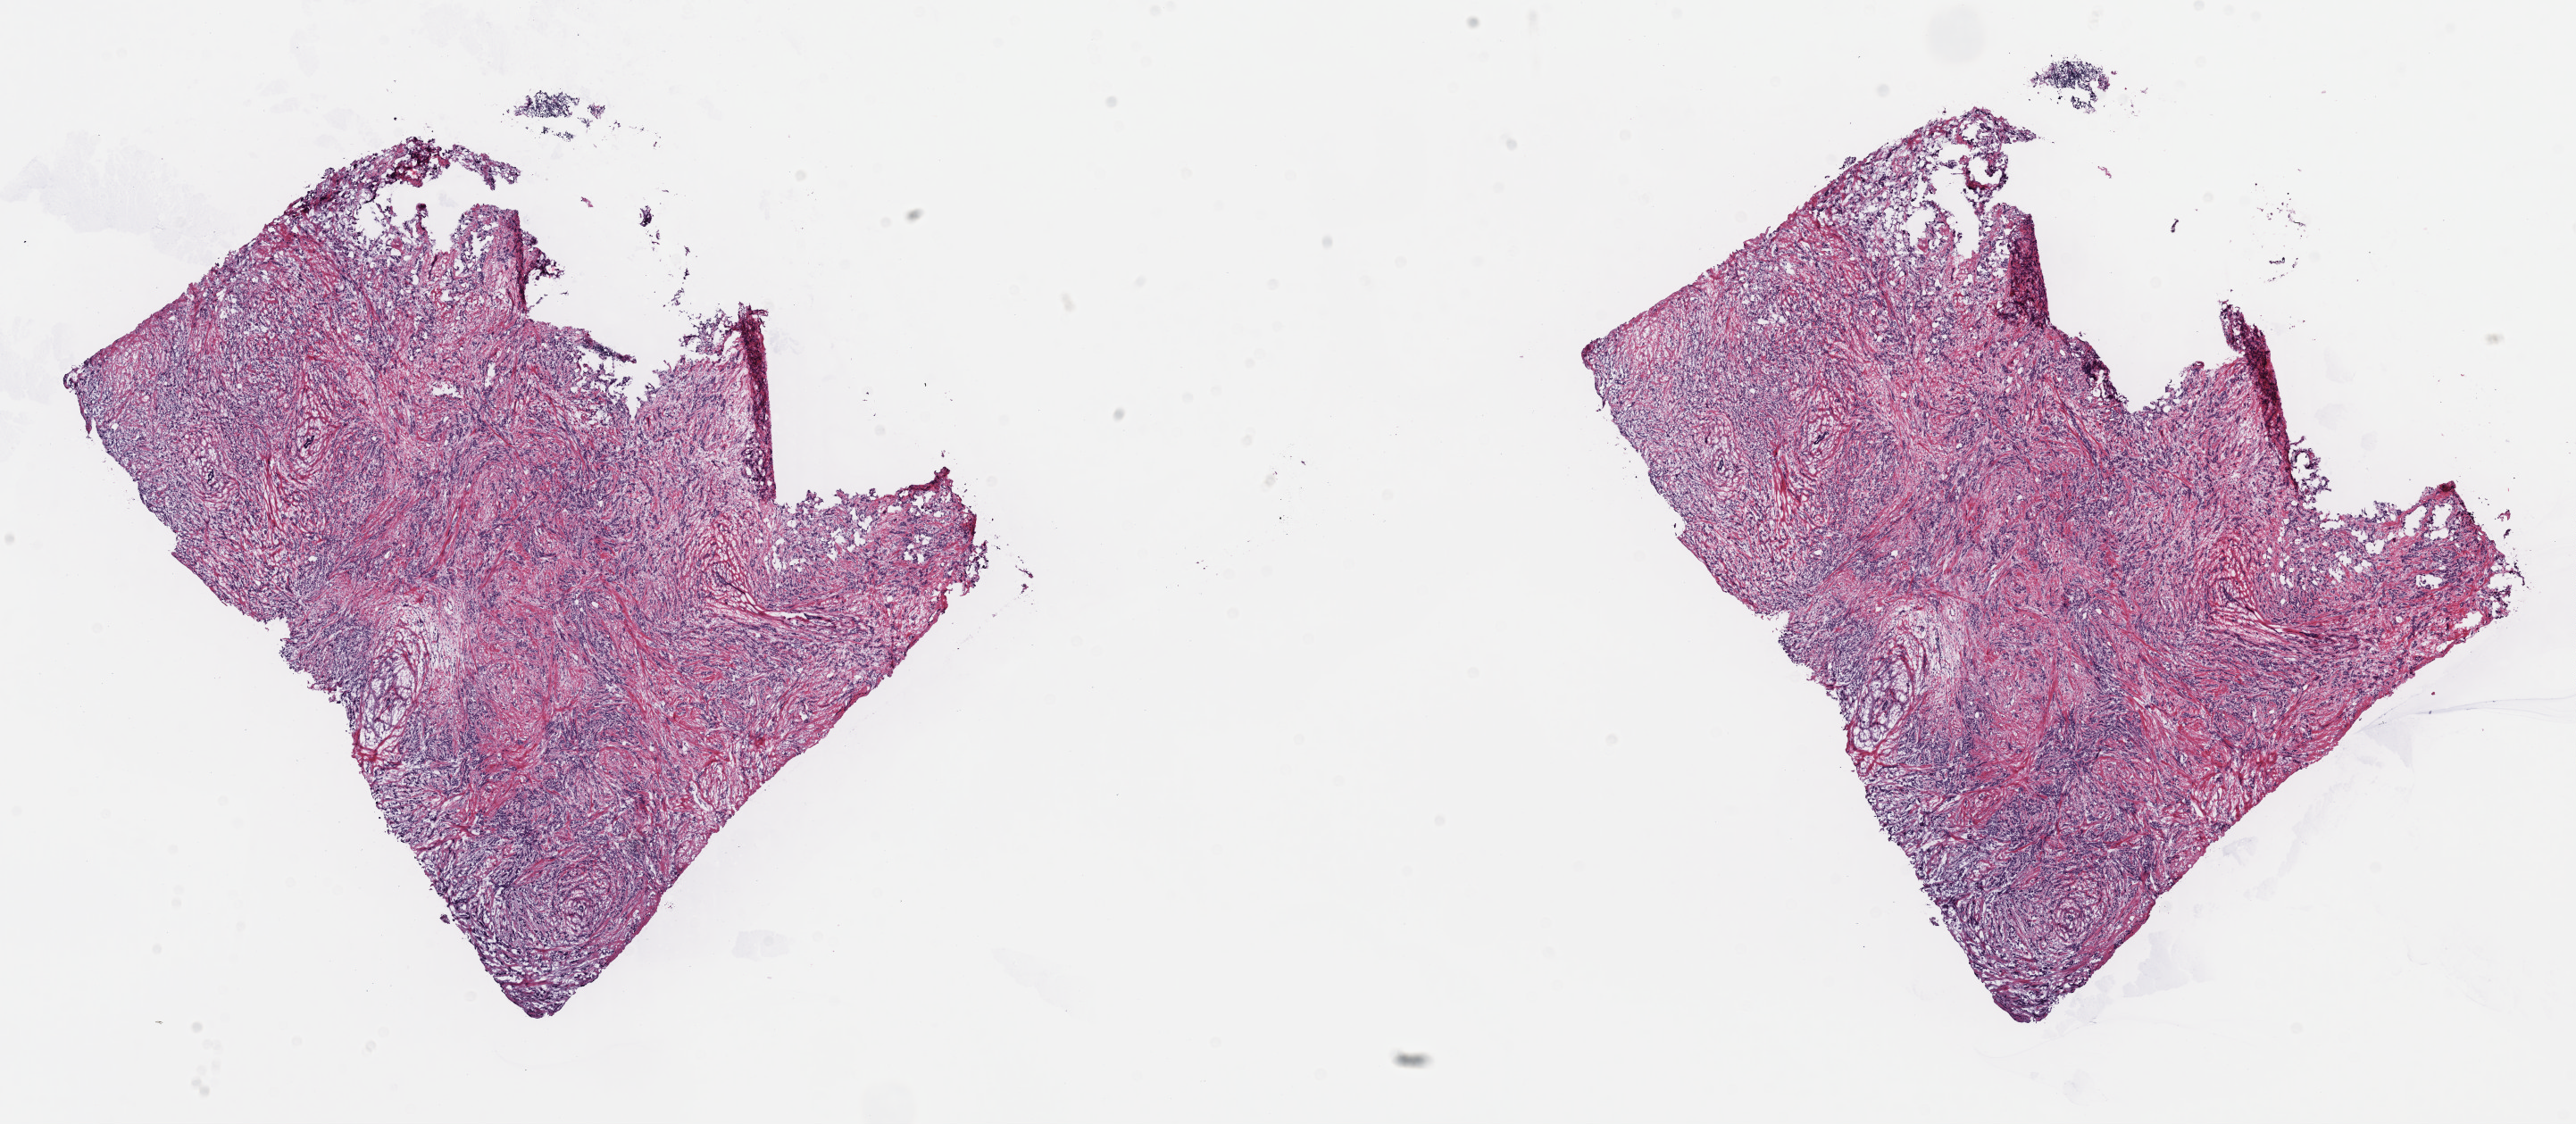
Whole-slide histology image, H&E-stained, shown as a low-resolution overview of the whole scanned area (about 22.8 x 9.9 mm, acquisition: 40x scan). Frozen section from the top of the tissue portion. Sample: primary tumour, breast. Patient: female, age at initial diagnosis 56 years. Pathologist review of this section (percent, as recorded): tumour cells 75%, tumour nuclei 80%, normal cells 0%, stromal cells 25%, necrosis 0%. Infiltration values recorded for this section: lymphocyte infiltration 1%, monocyte infiltration 0%, neutrophil infiltration 0%.
* AJCC pathologic stage: IIB
* histologic diagnosis: Lobular carcinoma, NOS
* lymph nodes positive (case pathology): 1 of 10 examined